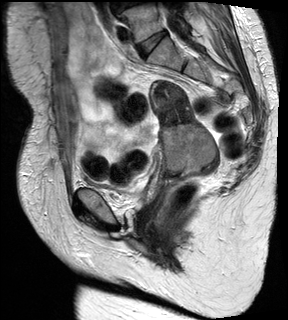
Pelvic MRI for cervical cancer, one sagittal slice; position 12 of 28 along the scan axis; T2-weighted; 1.5 T; TE 89 ms, TR 2740 ms; 4 mm slice thickness; 288 × 320 image matrix. Patient: female, 59 years.
Structures marked on this image (expert manual segmentation):
- uterus and cervix: box from (x=150, y=80) to (x=220, y=176) px